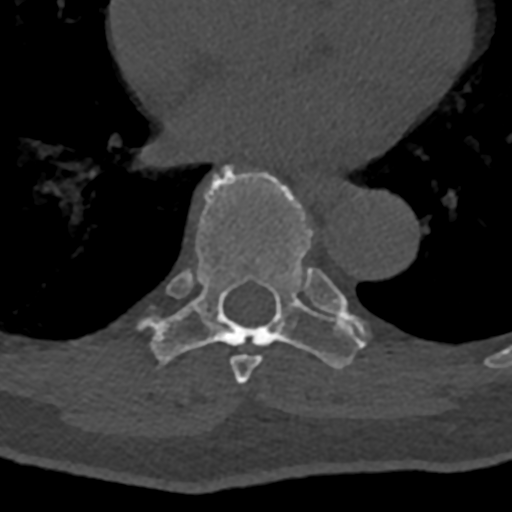
CT including the spine, one axial slice; slice 722 of 797 in the series (ordered by position); 120 kVp; bone window (W 1800 / L 400 HU); 0.5 mm slice thickness; 512 × 512 image matrix, field of view 160 × 160 mm. Patient: male, 74 years. From the clinical record (not read from this slice): primary cancer: renal; vertebrae with lytic lesions (as recorded): T10, L1, L2, L3, L4, L5.
Annotated regions visible in this slice (semi-automatic segmentation, software-assisted and operator-edited):
- T7 vertebra: bounding box <230,269,343,384> (left, top, right, bottom; pixels)
- T8 vertebra: <139,163,368,369>